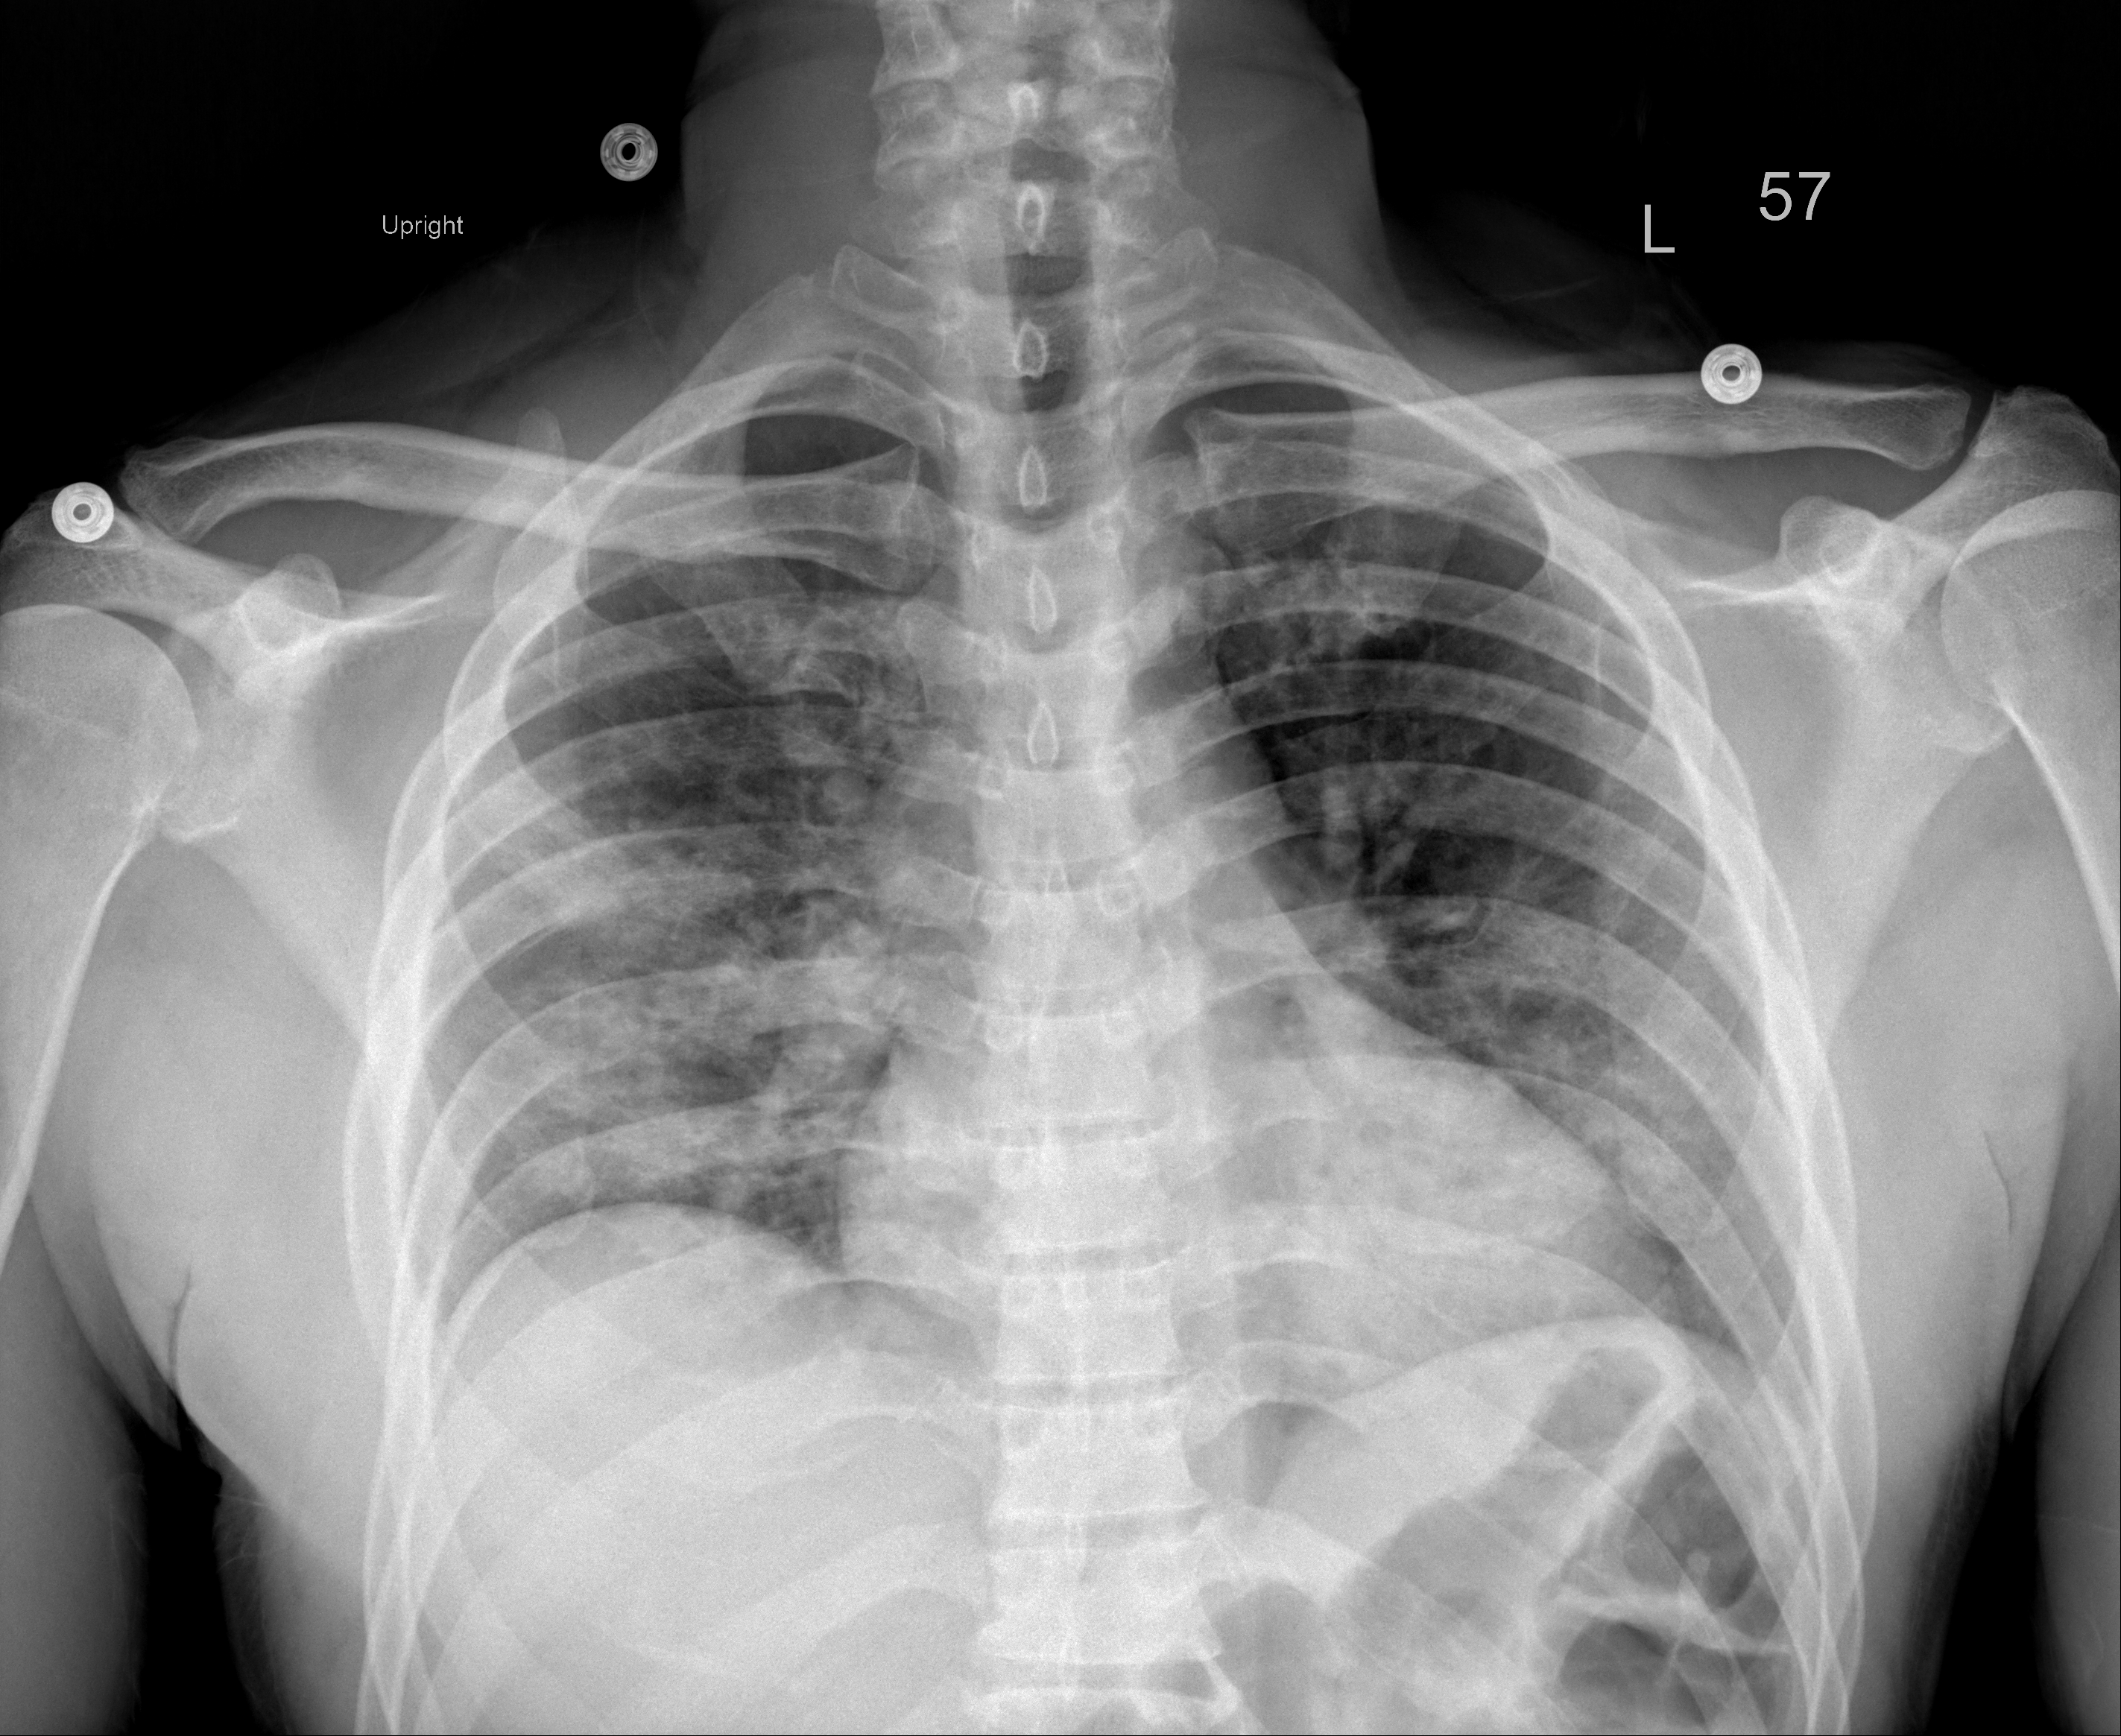
Chest X-ray (portable), AP projection. Male patient, age 49 years; imaged 3 days after the COVID-19 diagnosis.
Radiologist's key findings for this exam: Worsening consolidations noted in the lower lobes and mid right lung region.